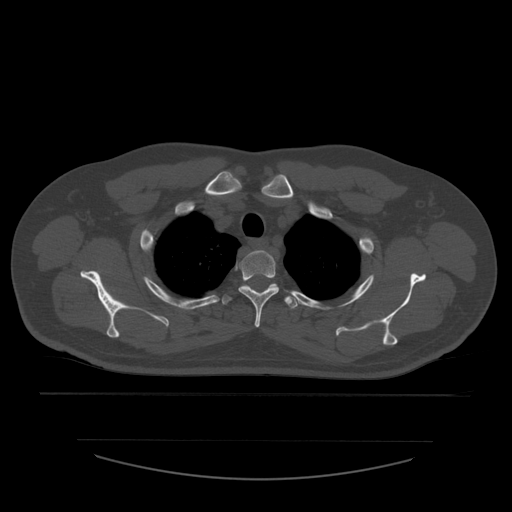
CT including the spine, one axial slice. Position 448 of 532 along the scan axis. 120 kVp. Bone window (W 1800 / L 400 HU). 1.25 mm slice thickness. 512 × 512 image matrix. Patient age 44 years. Case-level facts recorded for this patient, not image findings: primary cancer: soft tissue sarcoma.
Annotated regions visible in this slice (semi-automatically segmented with operator editing):
- T2 vertebra: bounding box (x1, y1, x2, y2) in pixels: (239, 250, 280, 328)
- T3 vertebra: (222, 284, 298, 309)